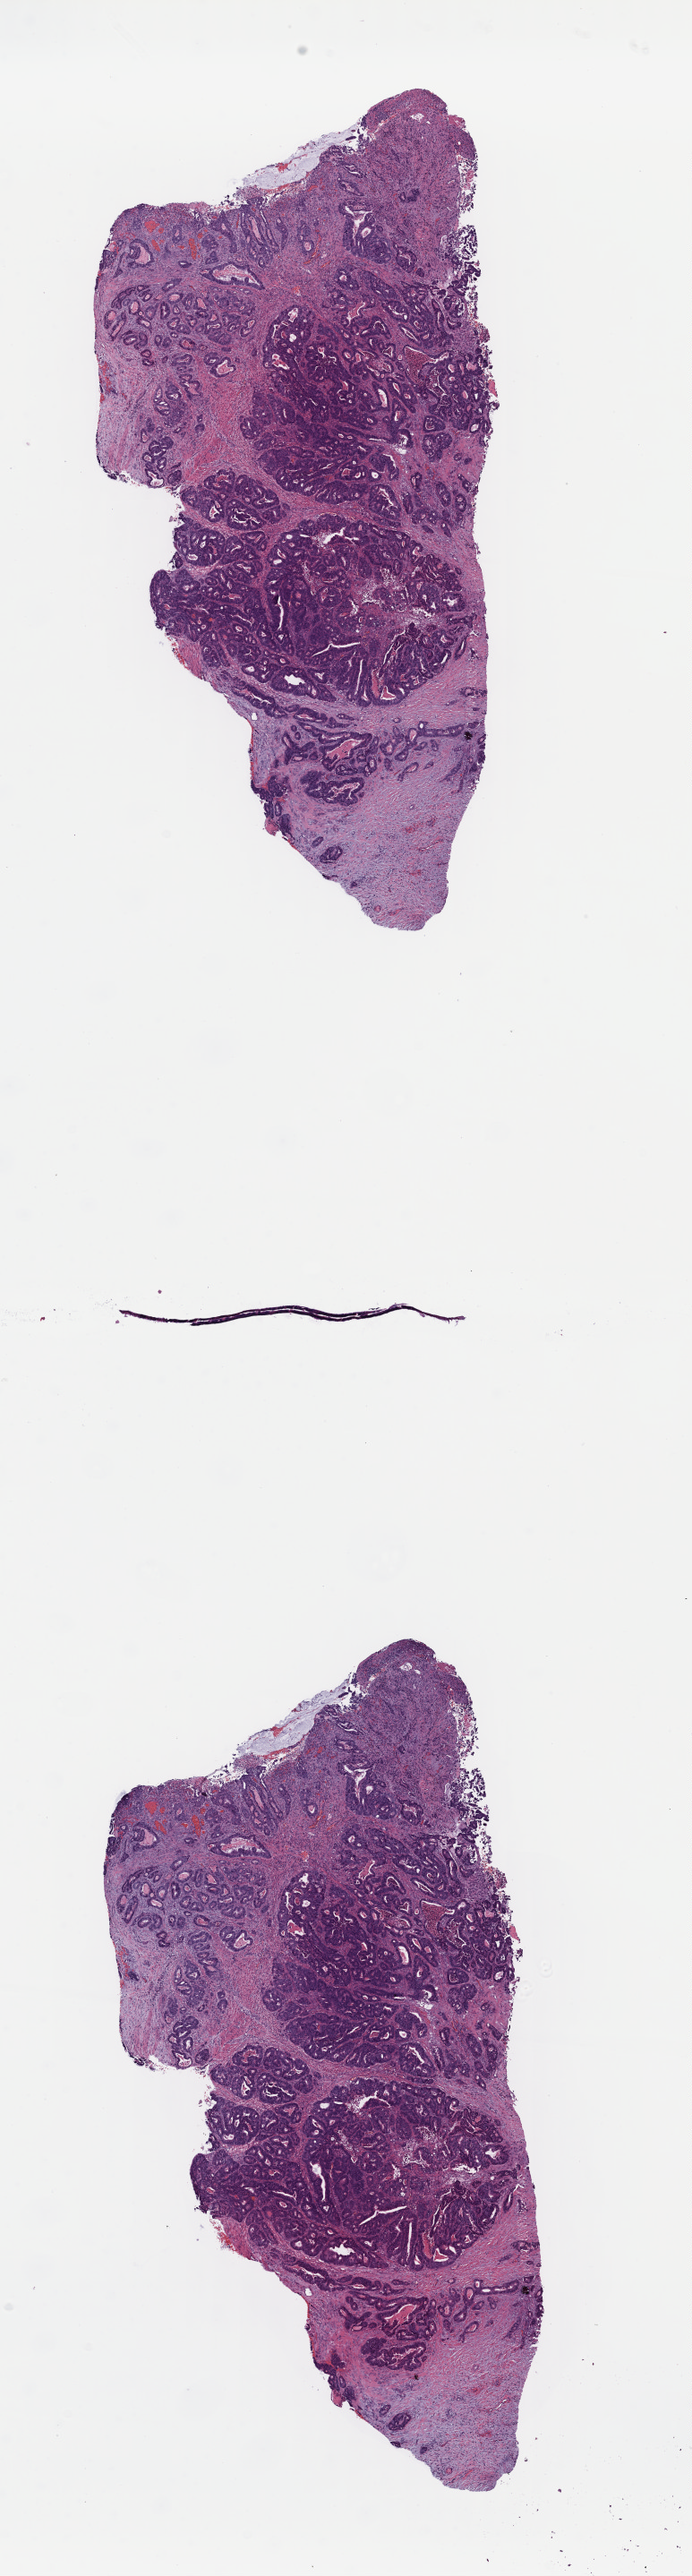
Whole-slide histology image, H&E — whole scanned area (about 6.1 x 22.7 mm) shown as a low-resolution overview. FFPE section. Colon, primary tumour sample. Male, age 59 years at initial diagnosis.
Lymph nodes positive (case pathology): 1 of 60 examined. AJCC pathologic stage: IIIB (7th edition). Diagnosis: Adenocarcinoma, NOS (transverse colon).